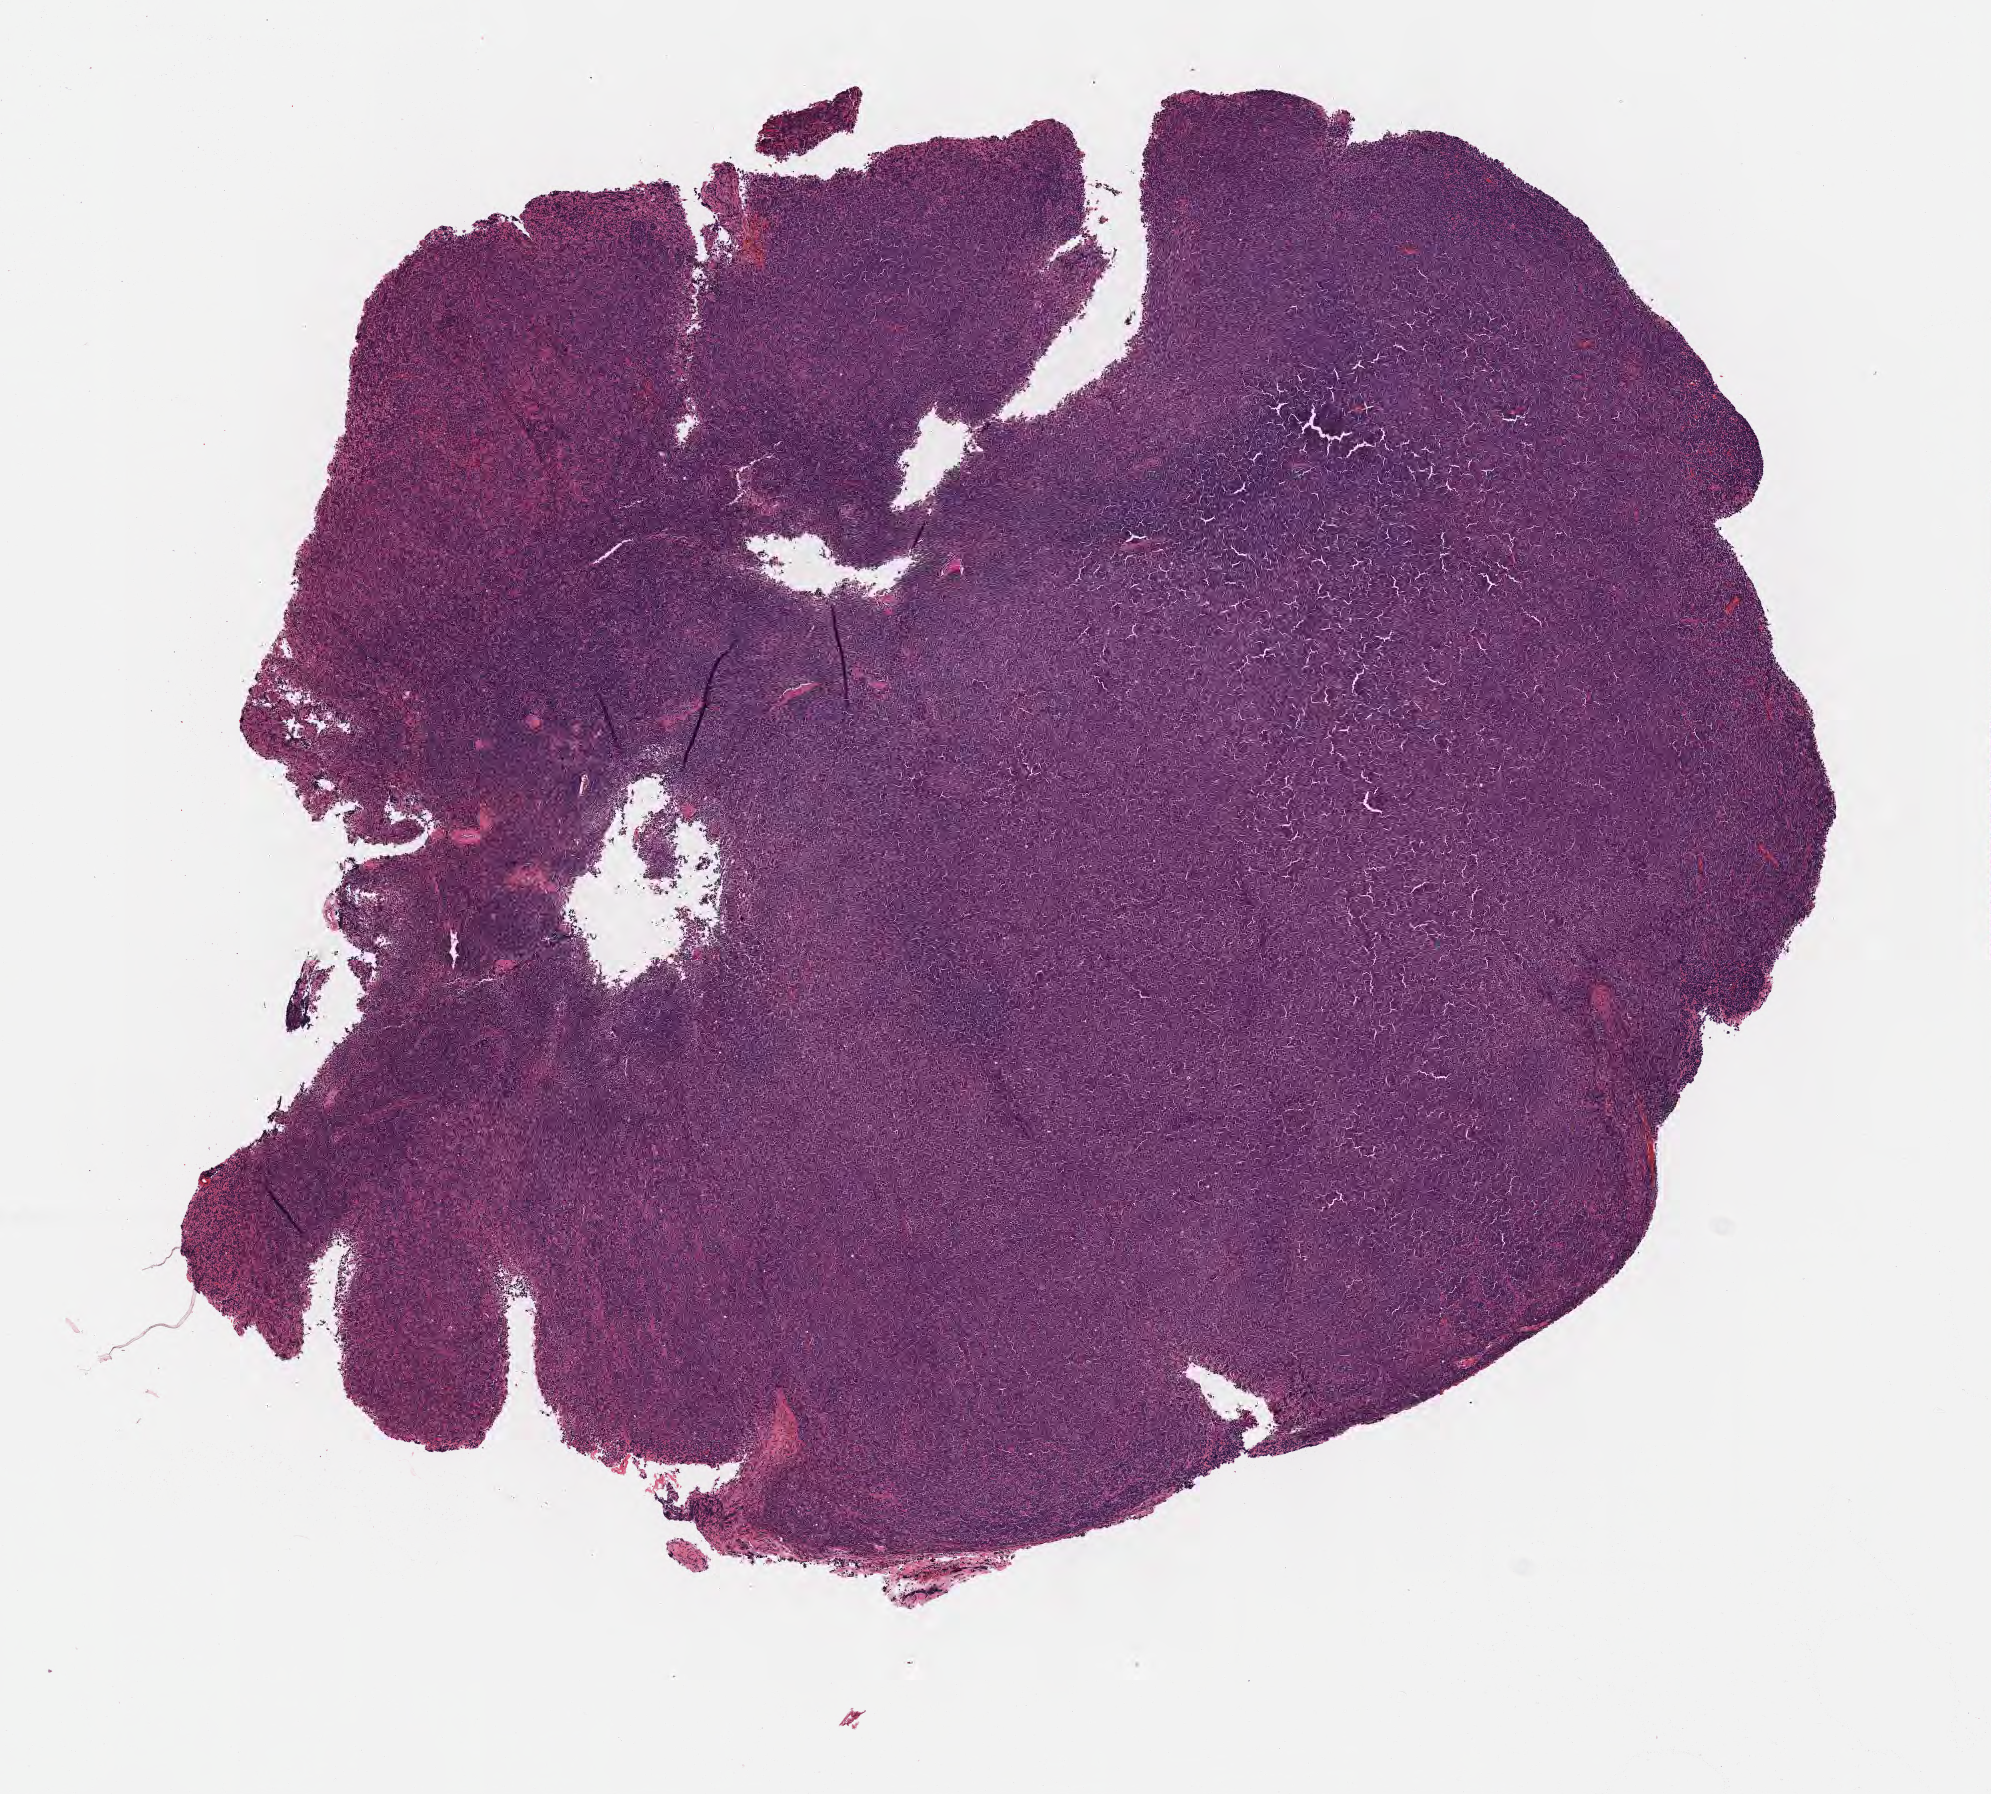
Hematoxylin and eosin (H&E) whole-slide image — a low-resolution overview of the entire scanned area, about 8.1 x 7.3 mm; tumor tissue; anatomic site: liver. Patient: male, age 46 years.
• diagnosis: Diffuse large B-cell lymphoma, NOS